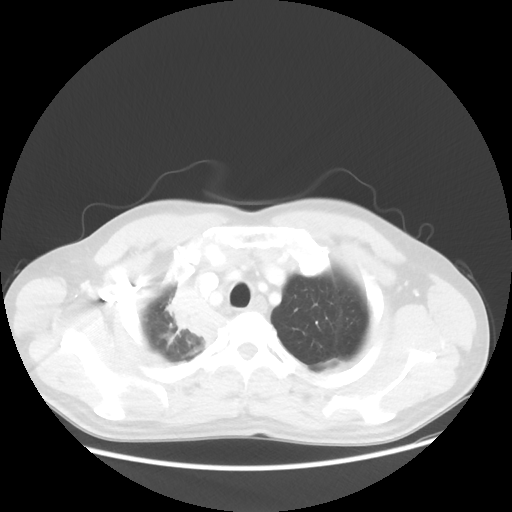
Chest CT, one axial slice. 100 kVp. Lung window (W 1500 / L -600 HU). 5 mm slice thickness. 512 × 512 image matrix, field of view 398 × 398 mm. Male patient, age 60 years. From the clinical record (not read from this slice): clinical TNM (as recorded): T2a N1 M0.
Outlined on this slice (rectangle marked by the reading radiologist):
- lung tumour (recorded histology: squamous cell carcinoma): bounding box (x1, y1, x2, y2) in pixels: (162, 276, 247, 359)